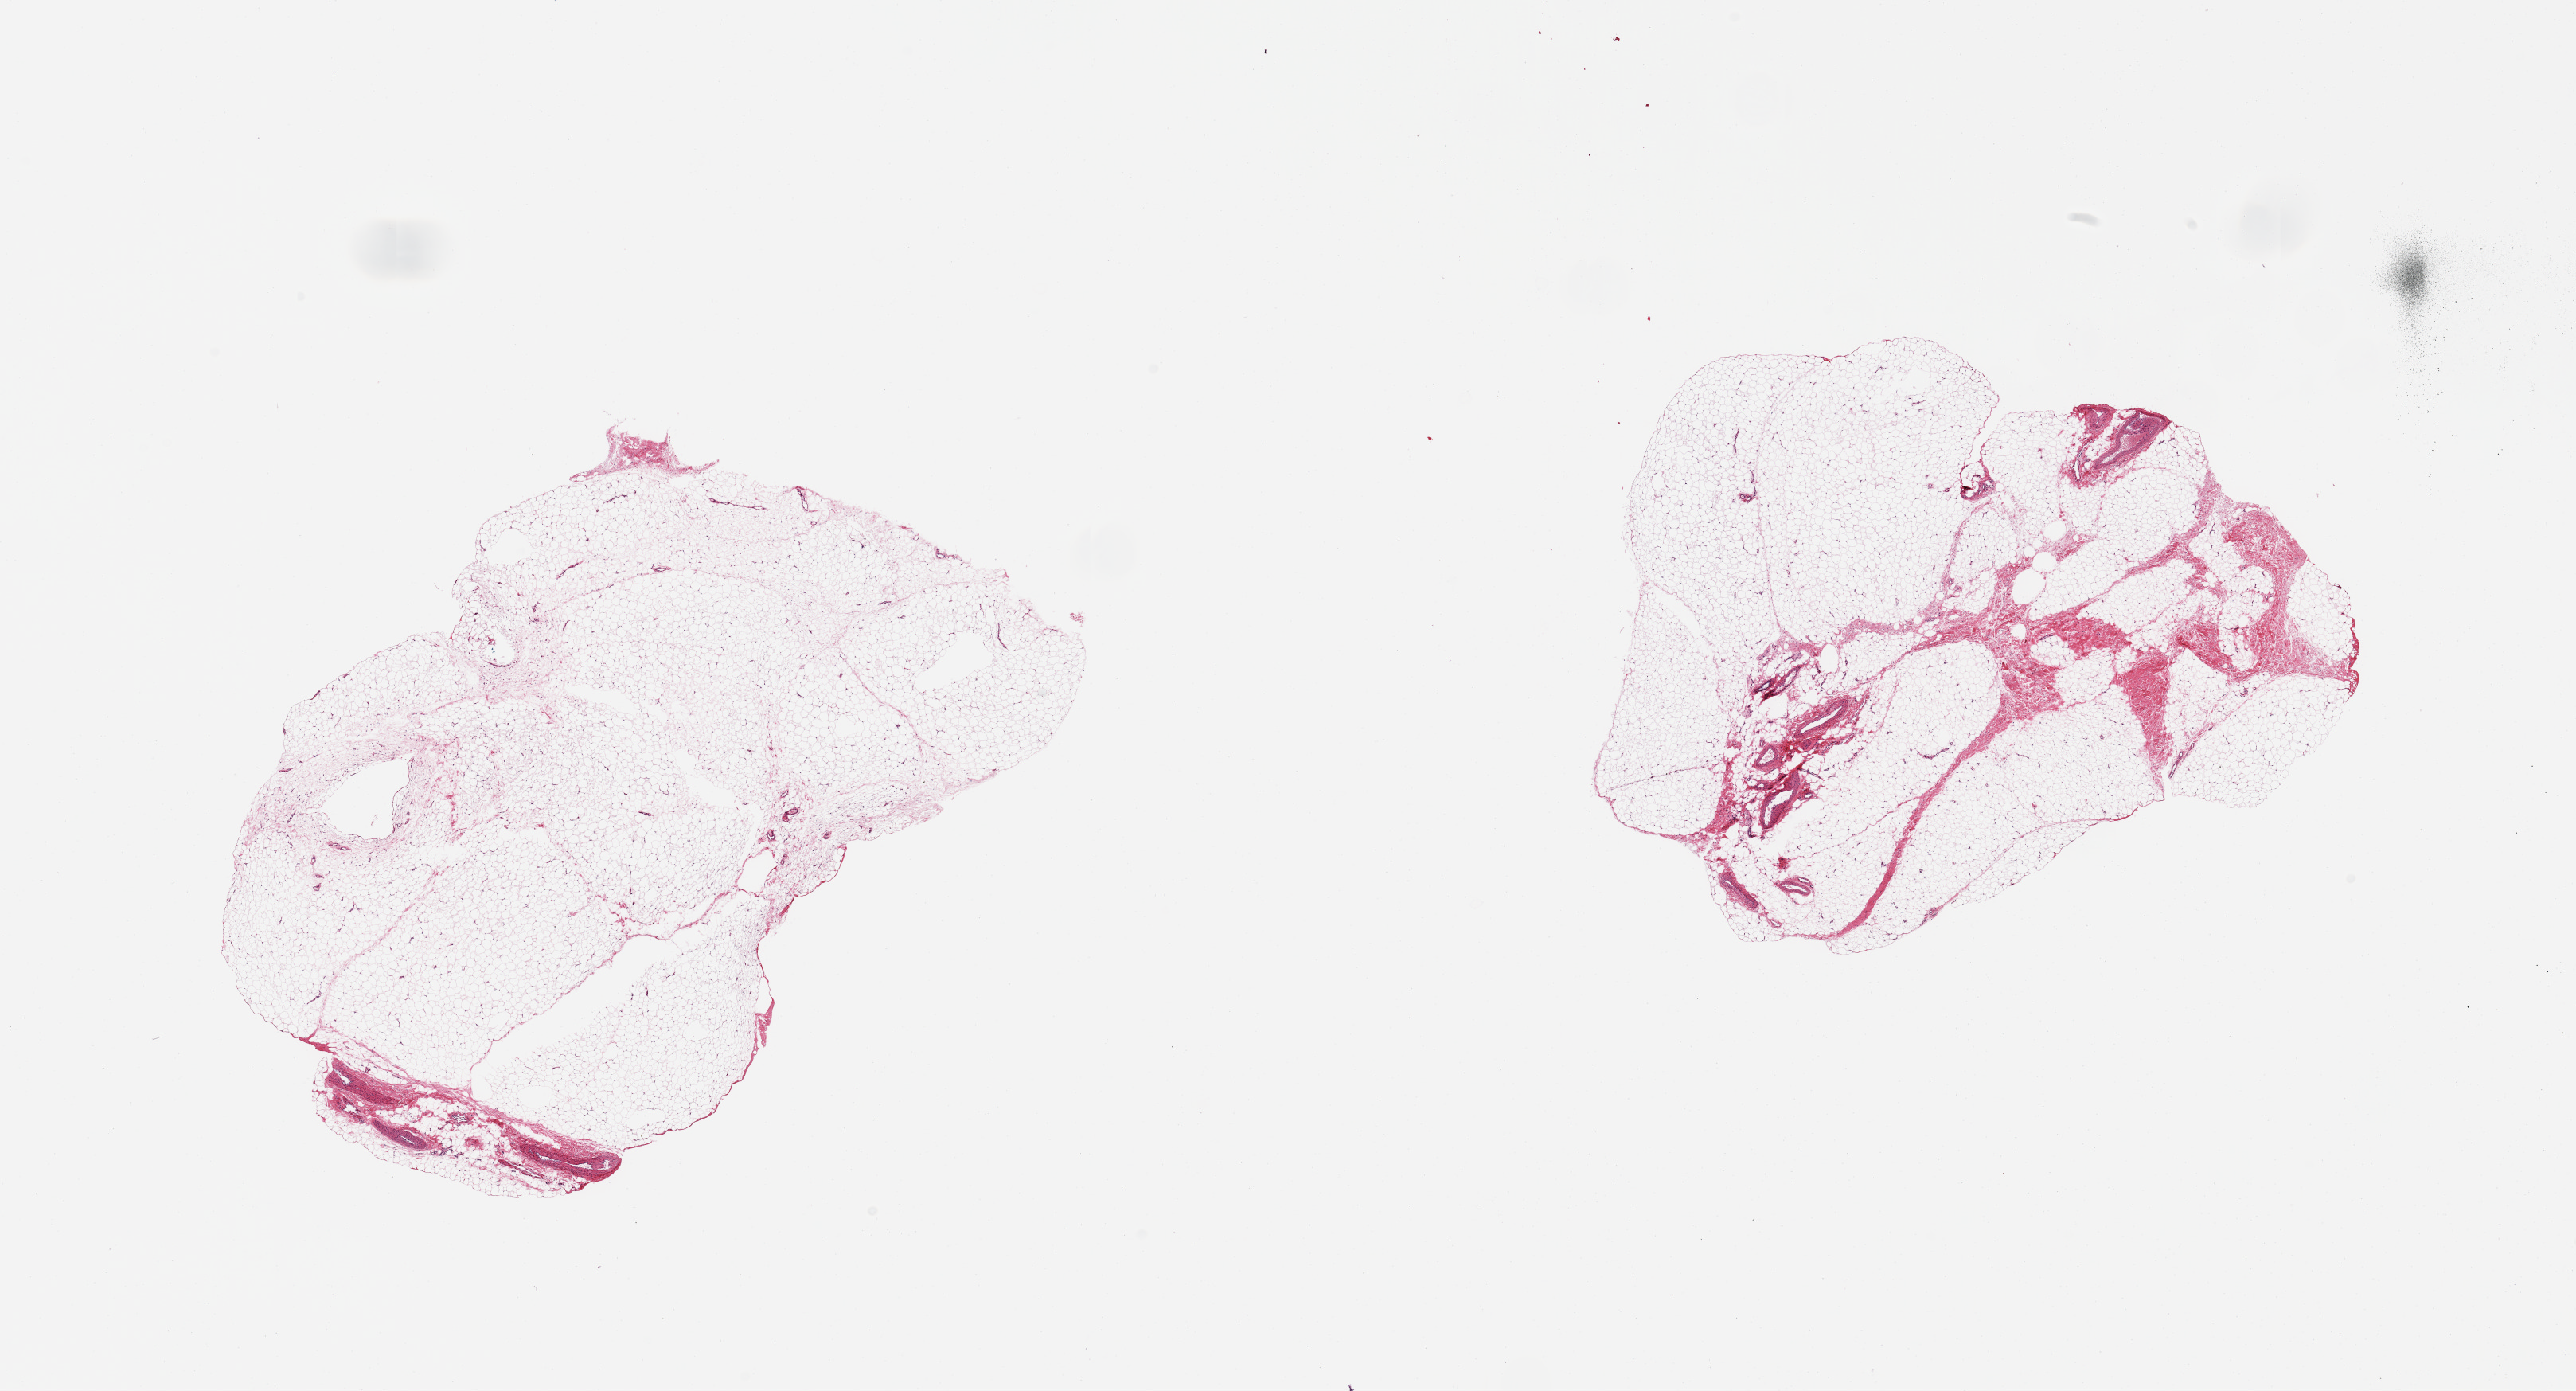
Digitized H&E-stained section, whole scanned area (about 25.6 x 13.8 mm, slide scanned at 20x) shown as a low-resolution overview. PAXgene-fixed paraffin-embedded (PFPE) section. Section of adipose tissue (target tissue). Tissue donor sample.
Reviewer comment on this tissue sample: 2 pieces; predominantly fat, 5 and 10-15% fibrous tissue/larger vessels.